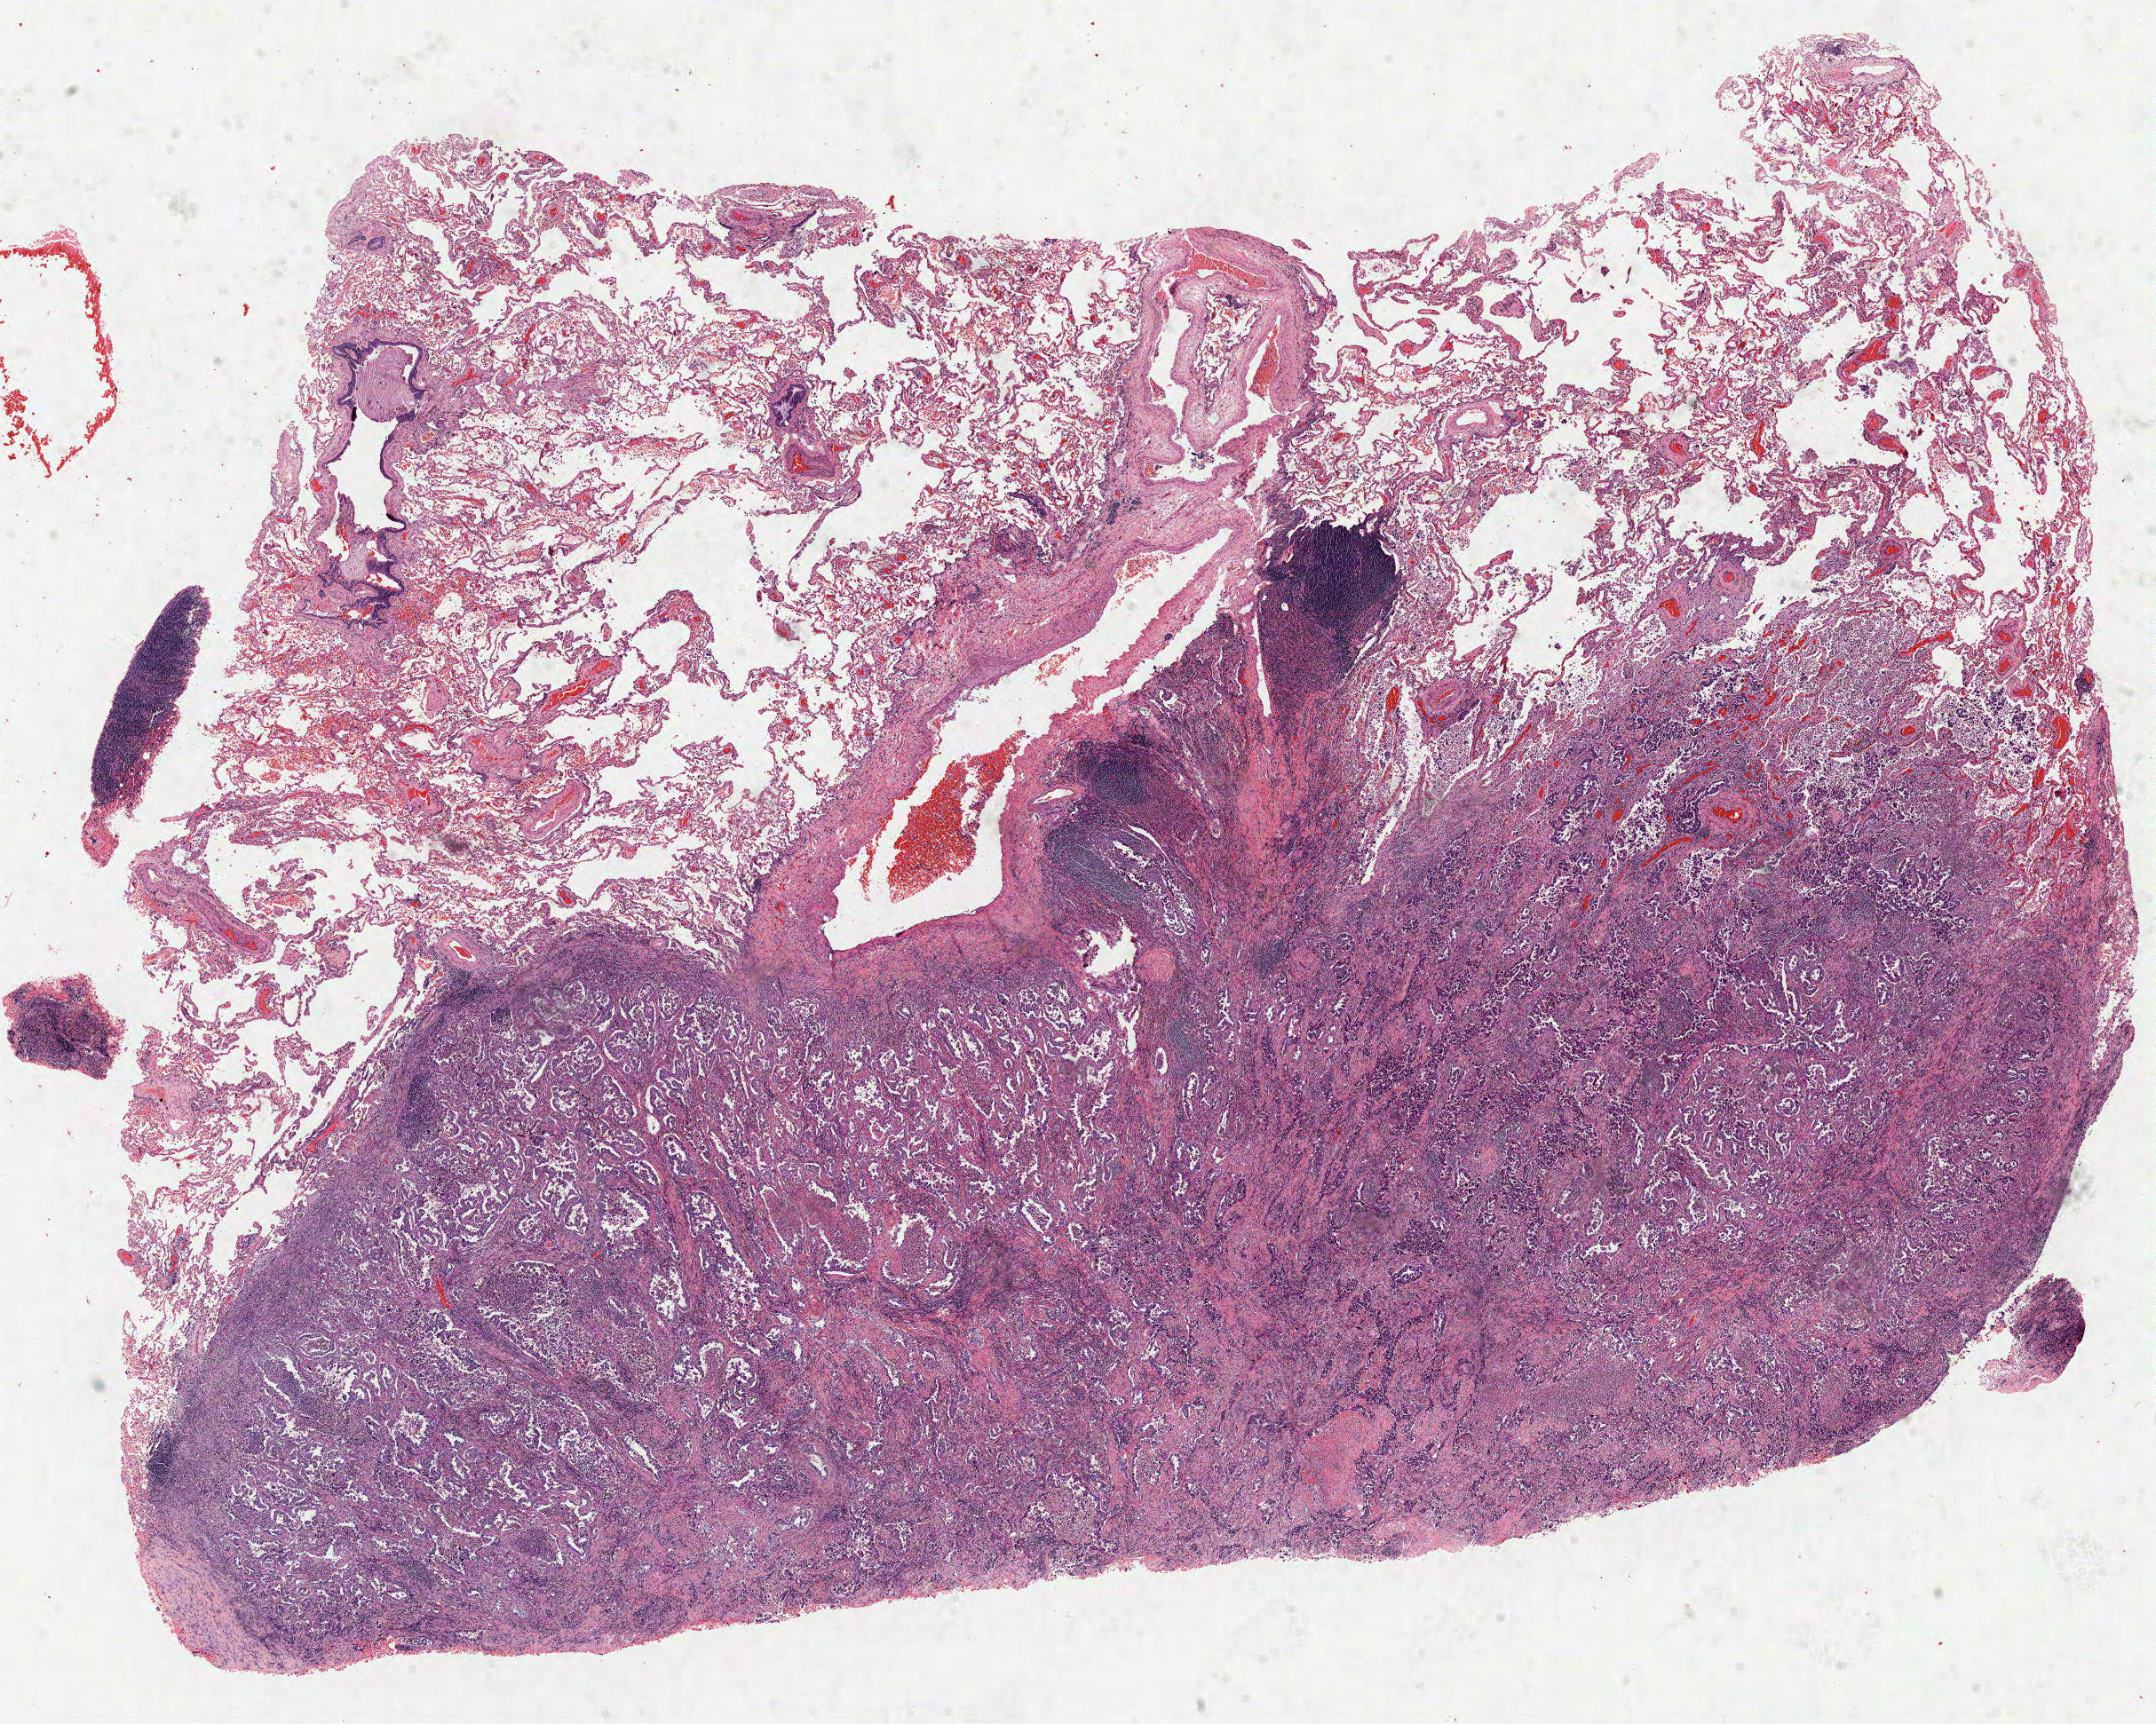
Whole-slide histology image, Hematoxylin and eosin (H&E) stained — whole scanned area (about 19.6 x 15.7 mm, acquisition: 40x scan) shown as a low-resolution overview; formalin-fixed paraffin-embedded (FFPE) diagnostic section; lung, primary tumour sample. Female, age 73 years at initial diagnosis.
* histologic diagnosis: Adenocarcinoma, NOS (upper lobe, lung)
* TNM: T1b N0 M0
* AJCC pathologic stage: IA (7th edition)
* laterality: right